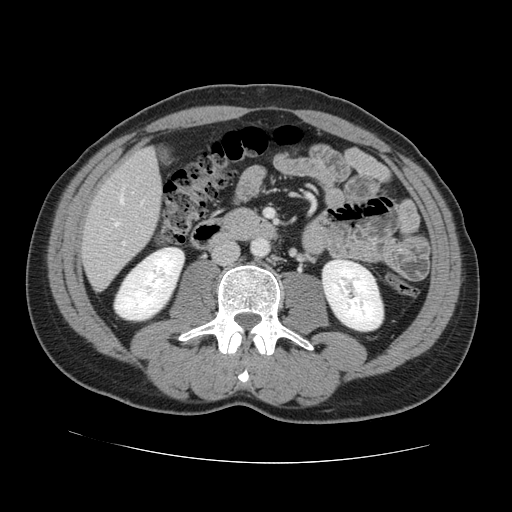
Contrast-enhanced abdominal CT, one axial slice; position 36 of 131 along the scan axis; intravenous contrast given; soft-tissue window (W 400 / L 40 HU); 512 × 512 image matrix. Male patient, age 40 years. Case-level facts recorded for this patient, not image findings: diagnosis: colorectal cancer liver metastases, imaged before liver resection; multiple liver metastases: yes; largest metastasis: 2.9 cm; disease in both lobes: yes.
Annotated regions visible in this slice (outlined manually by an expert reader):
- hepatic veins: bounding box [x1, y1, x2, y2] px = [115, 194, 123, 226]
- liver: [82, 149, 162, 289]
- planned liver remnant (the part of the liver to remain after resection): [139, 149, 156, 162]
- portal vein (with intrahepatic branches): [123, 242, 126, 245]